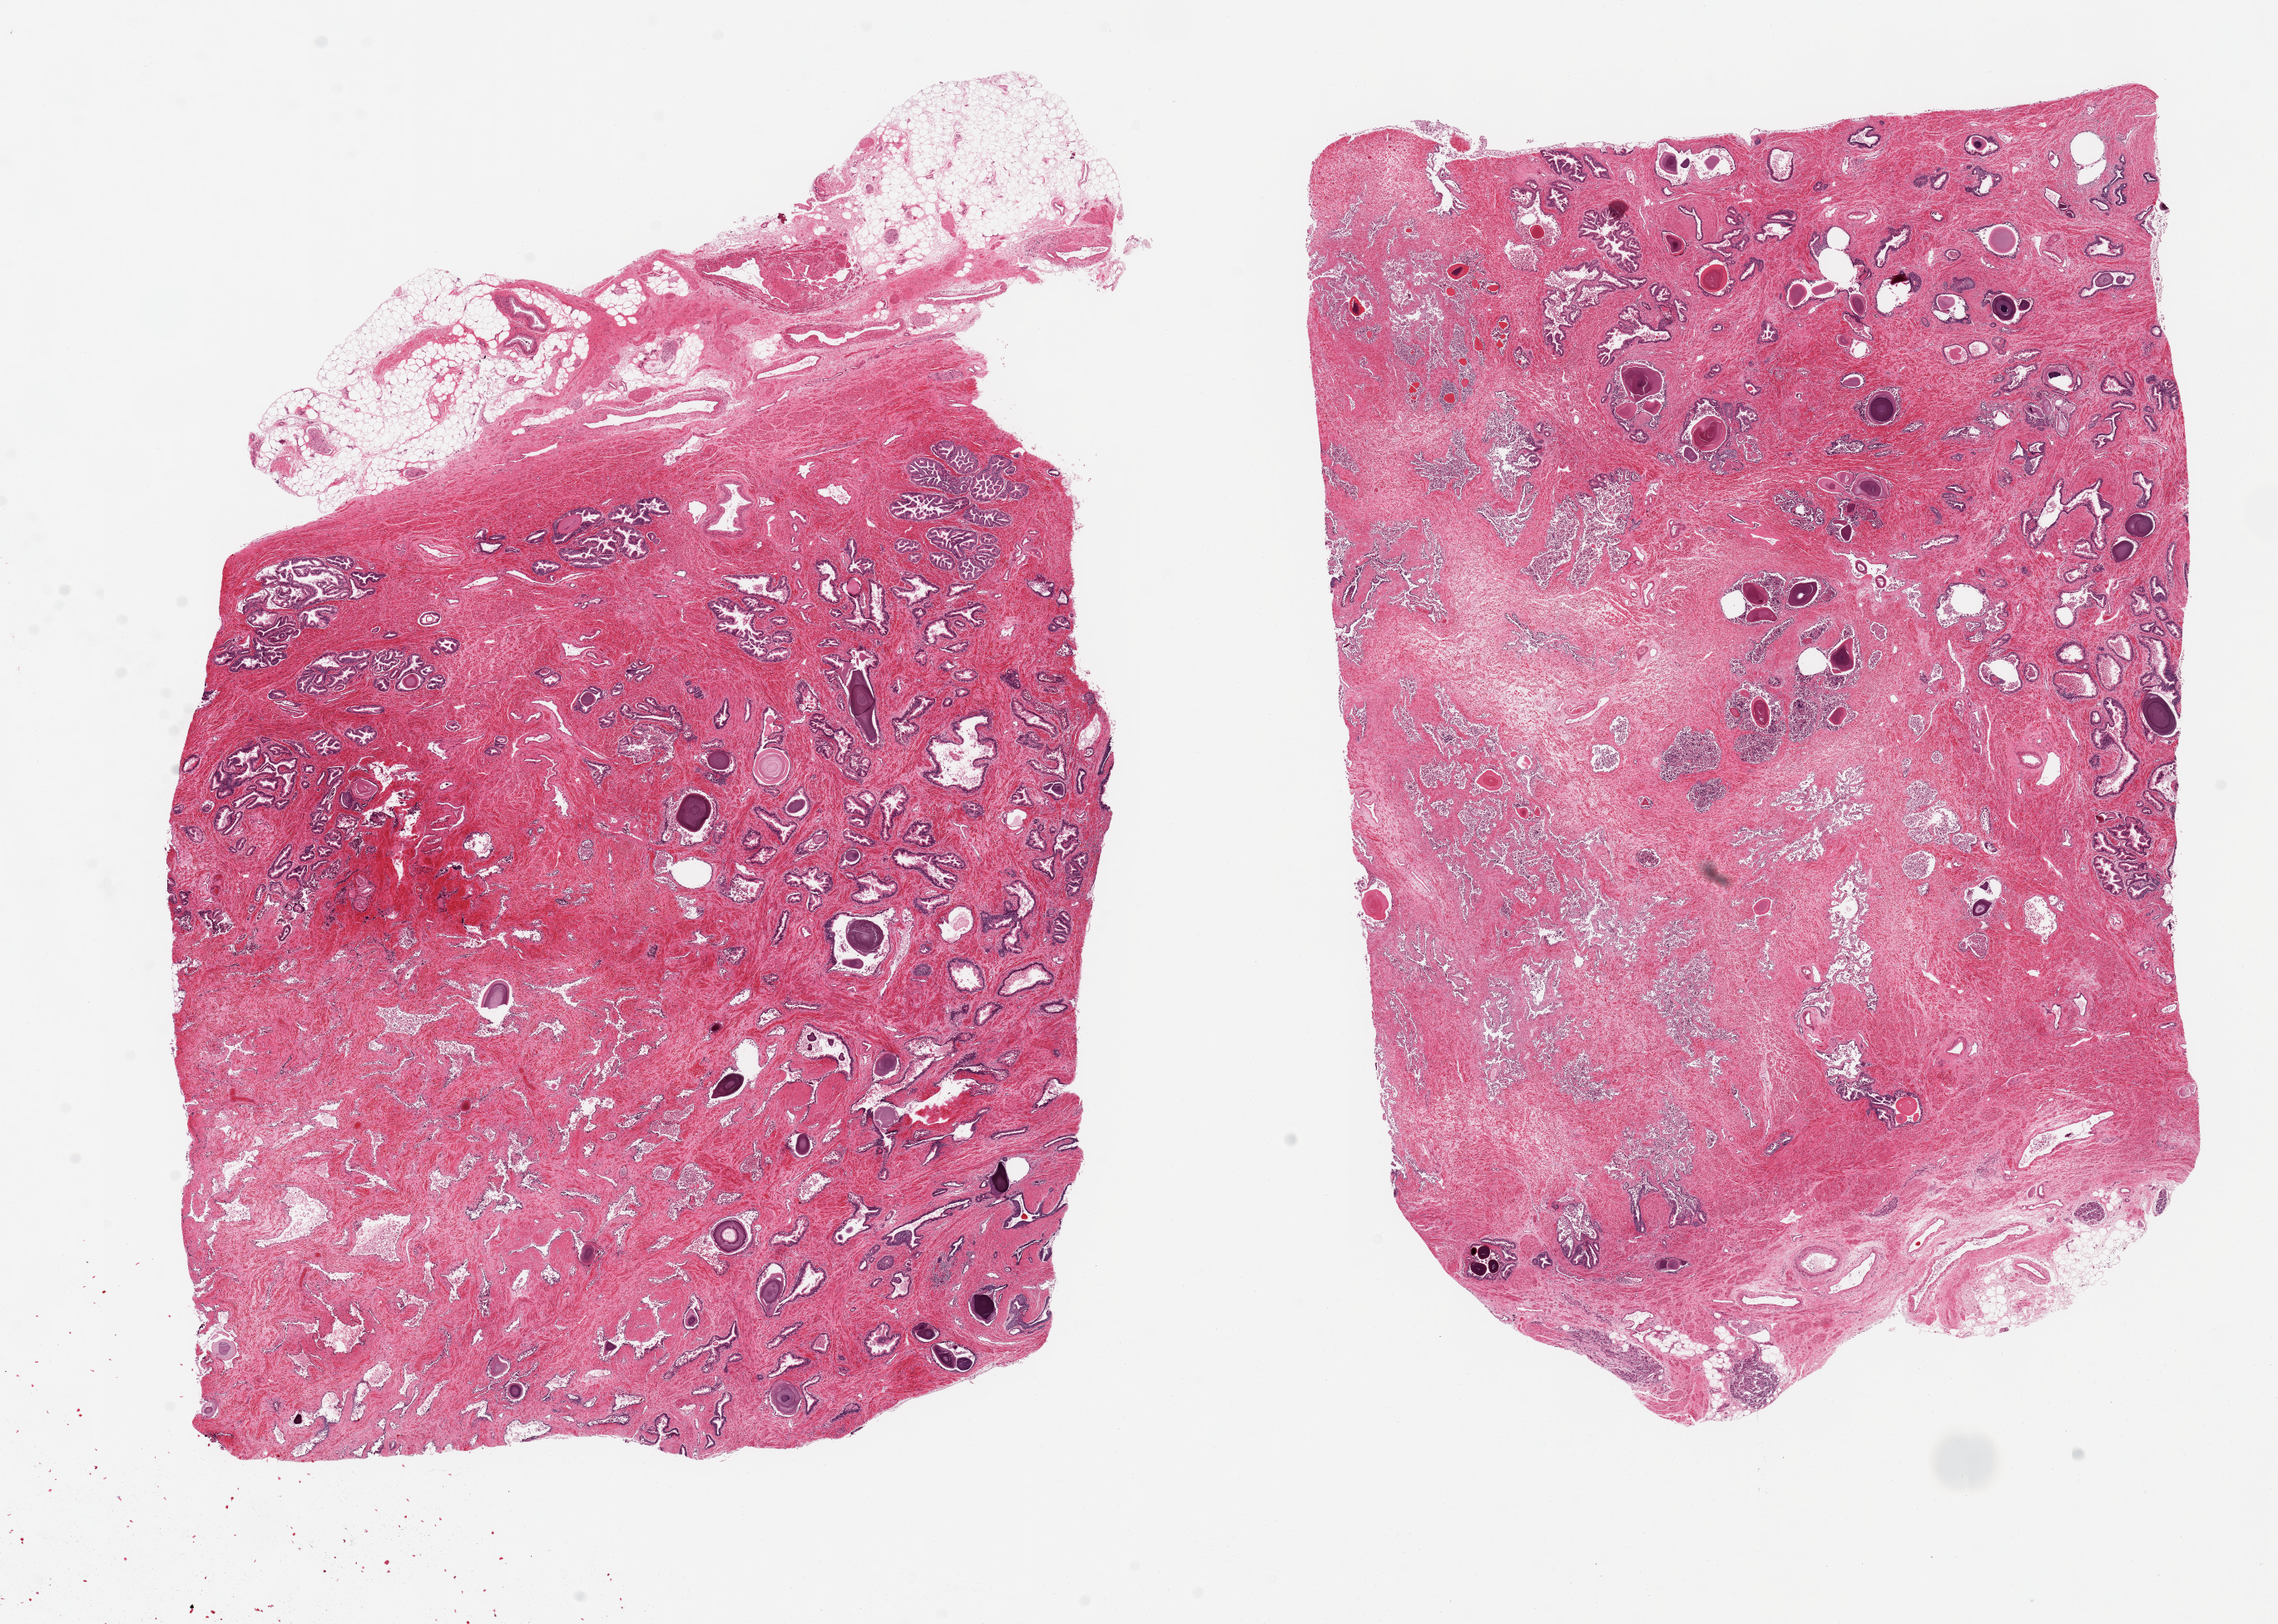
Digitized hematoxylin and eosin (H&E)-stained section — low-resolution overview of the scanned area, about 21.7 x 15.4 mm, PAXgene-fixed, paraffin-embedded tissue, sampled site (target tissue): prostate, donor tissue sample.
Review note (as recorded): 2 pieces, 13x8.5 & 12.5x8mm; Glands severely autolyzed; stroma moderately. 2mm adipose on edge of 1 piece.